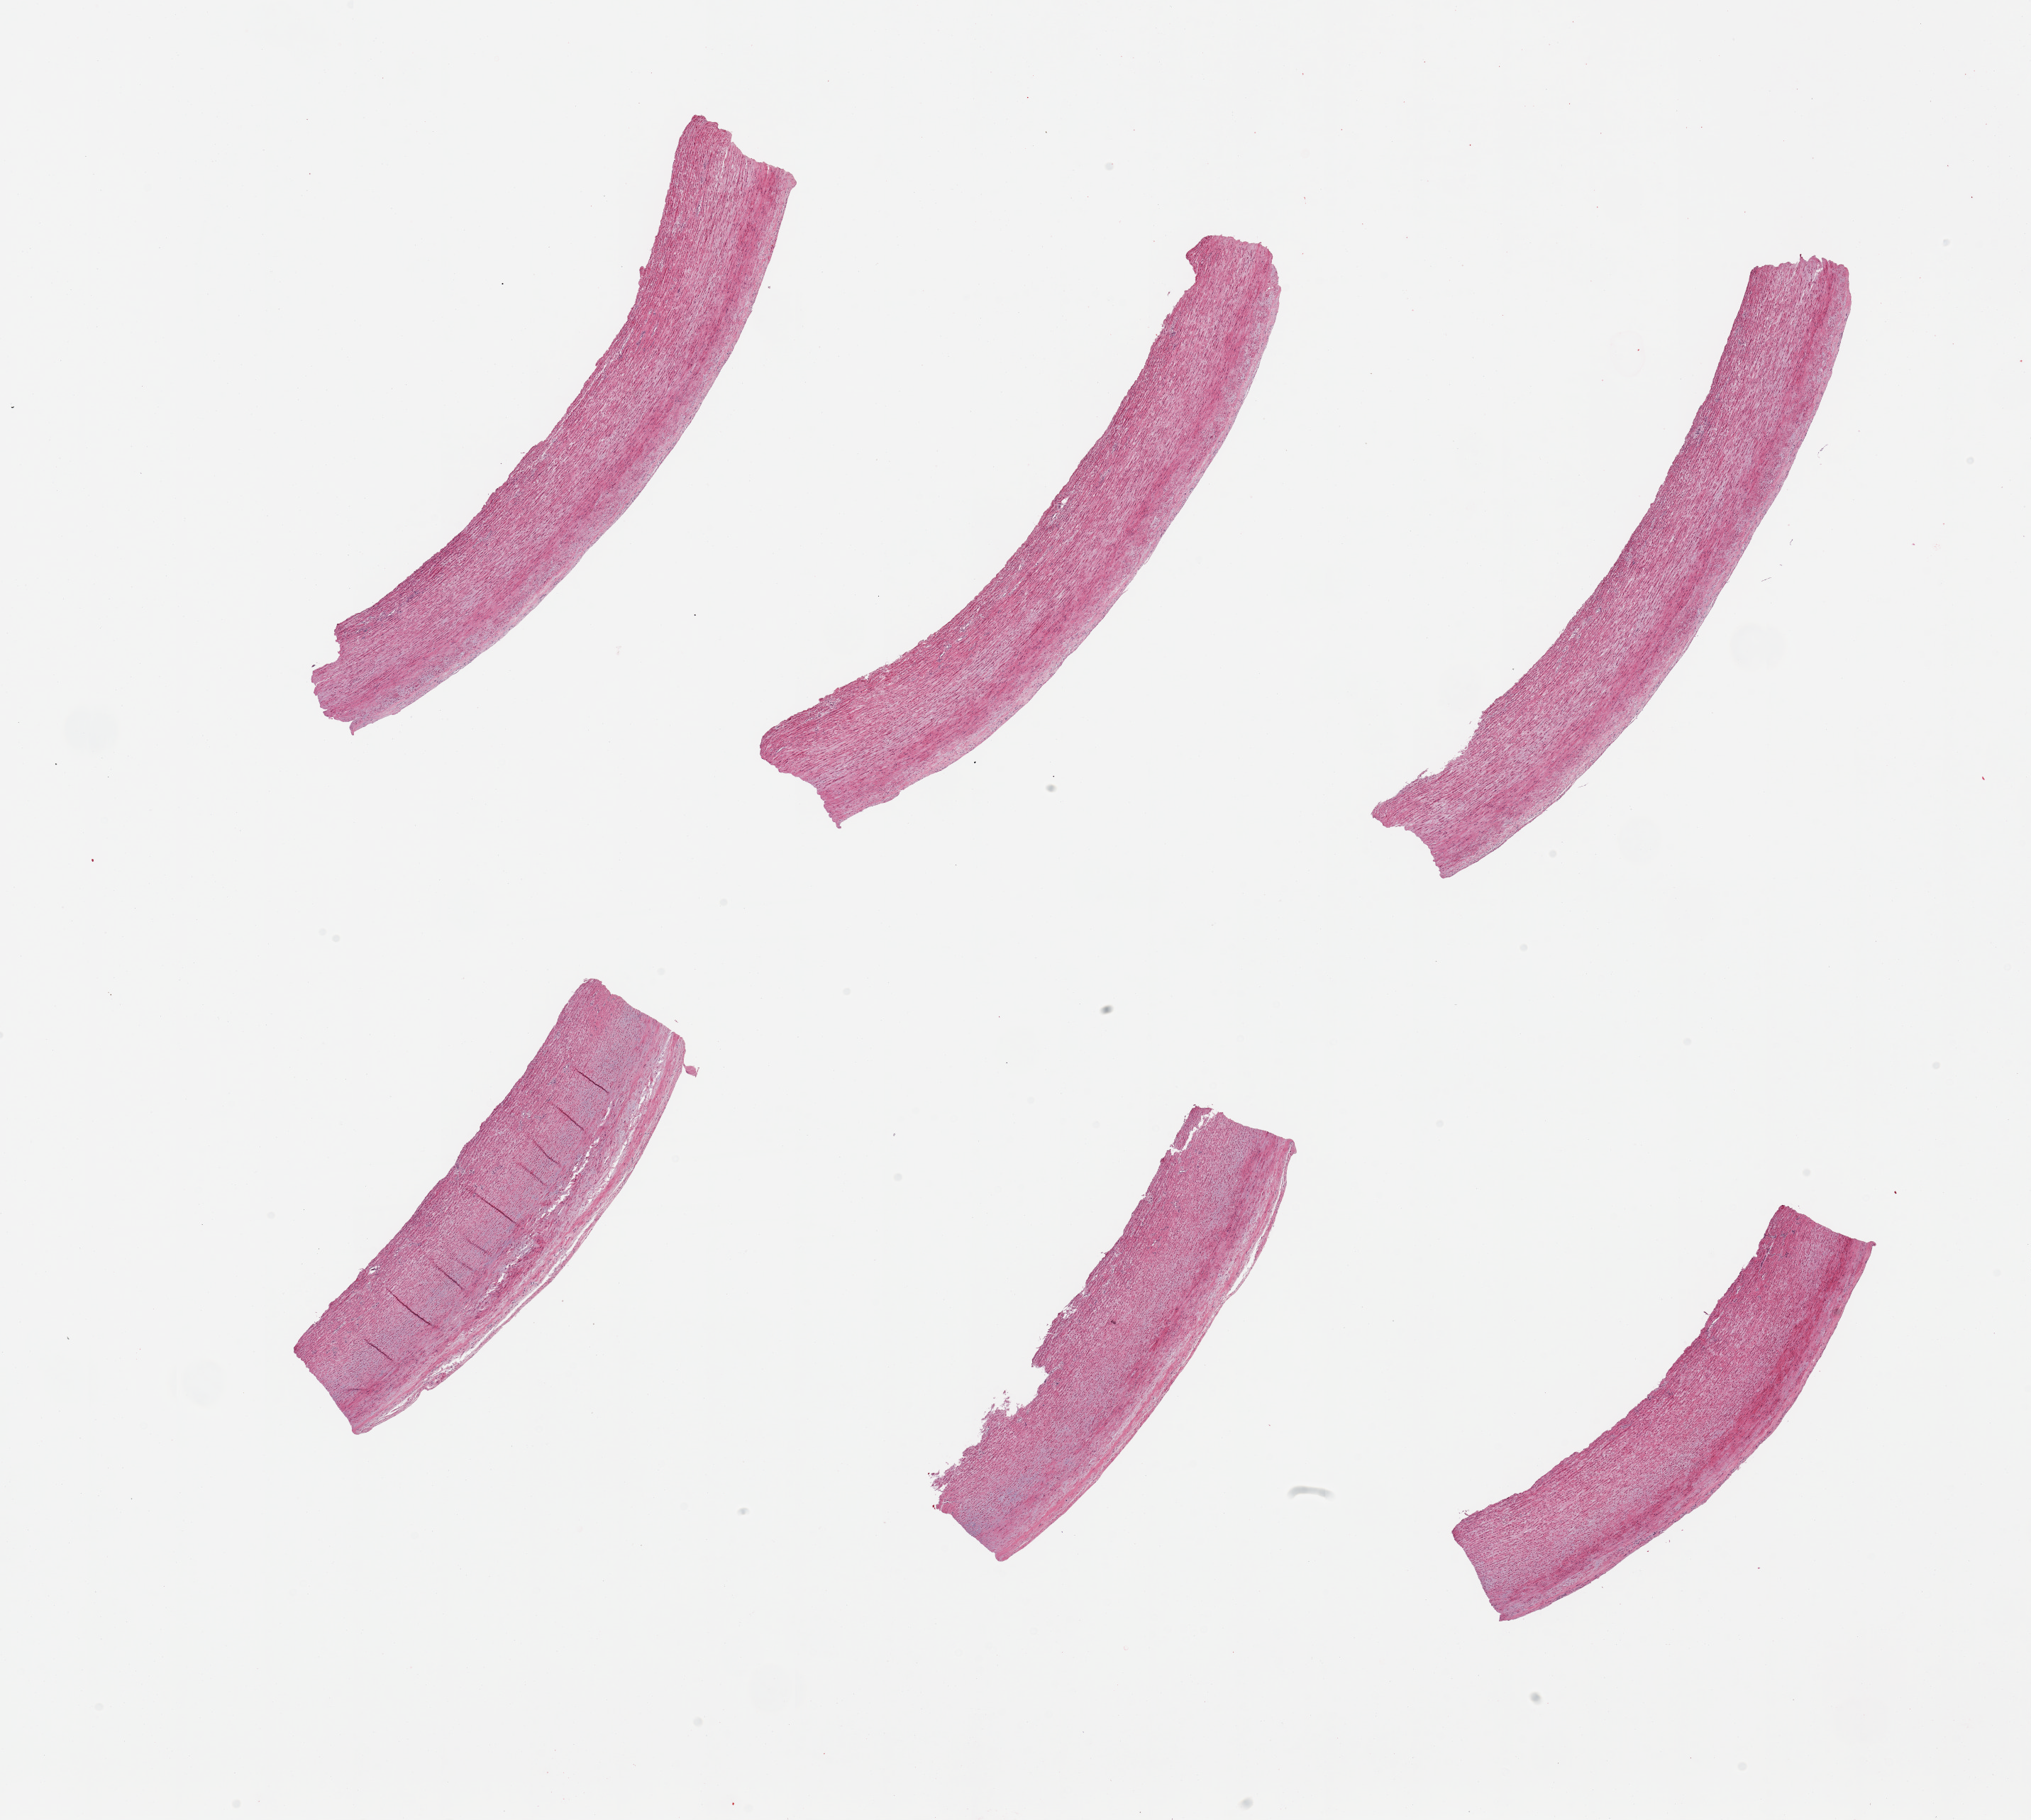
Digitized haematoxylin and eosin-stained section — low-resolution overview of the scanned area, about 22.6 x 20.3 mm. PAXgene-fixed, paraffin-embedded tissue. Sampled site (target tissue): aorta. Tissue donor sample.
• pathologist's review note for this sample: 6 pieces, atherosi up to ~0.5mm